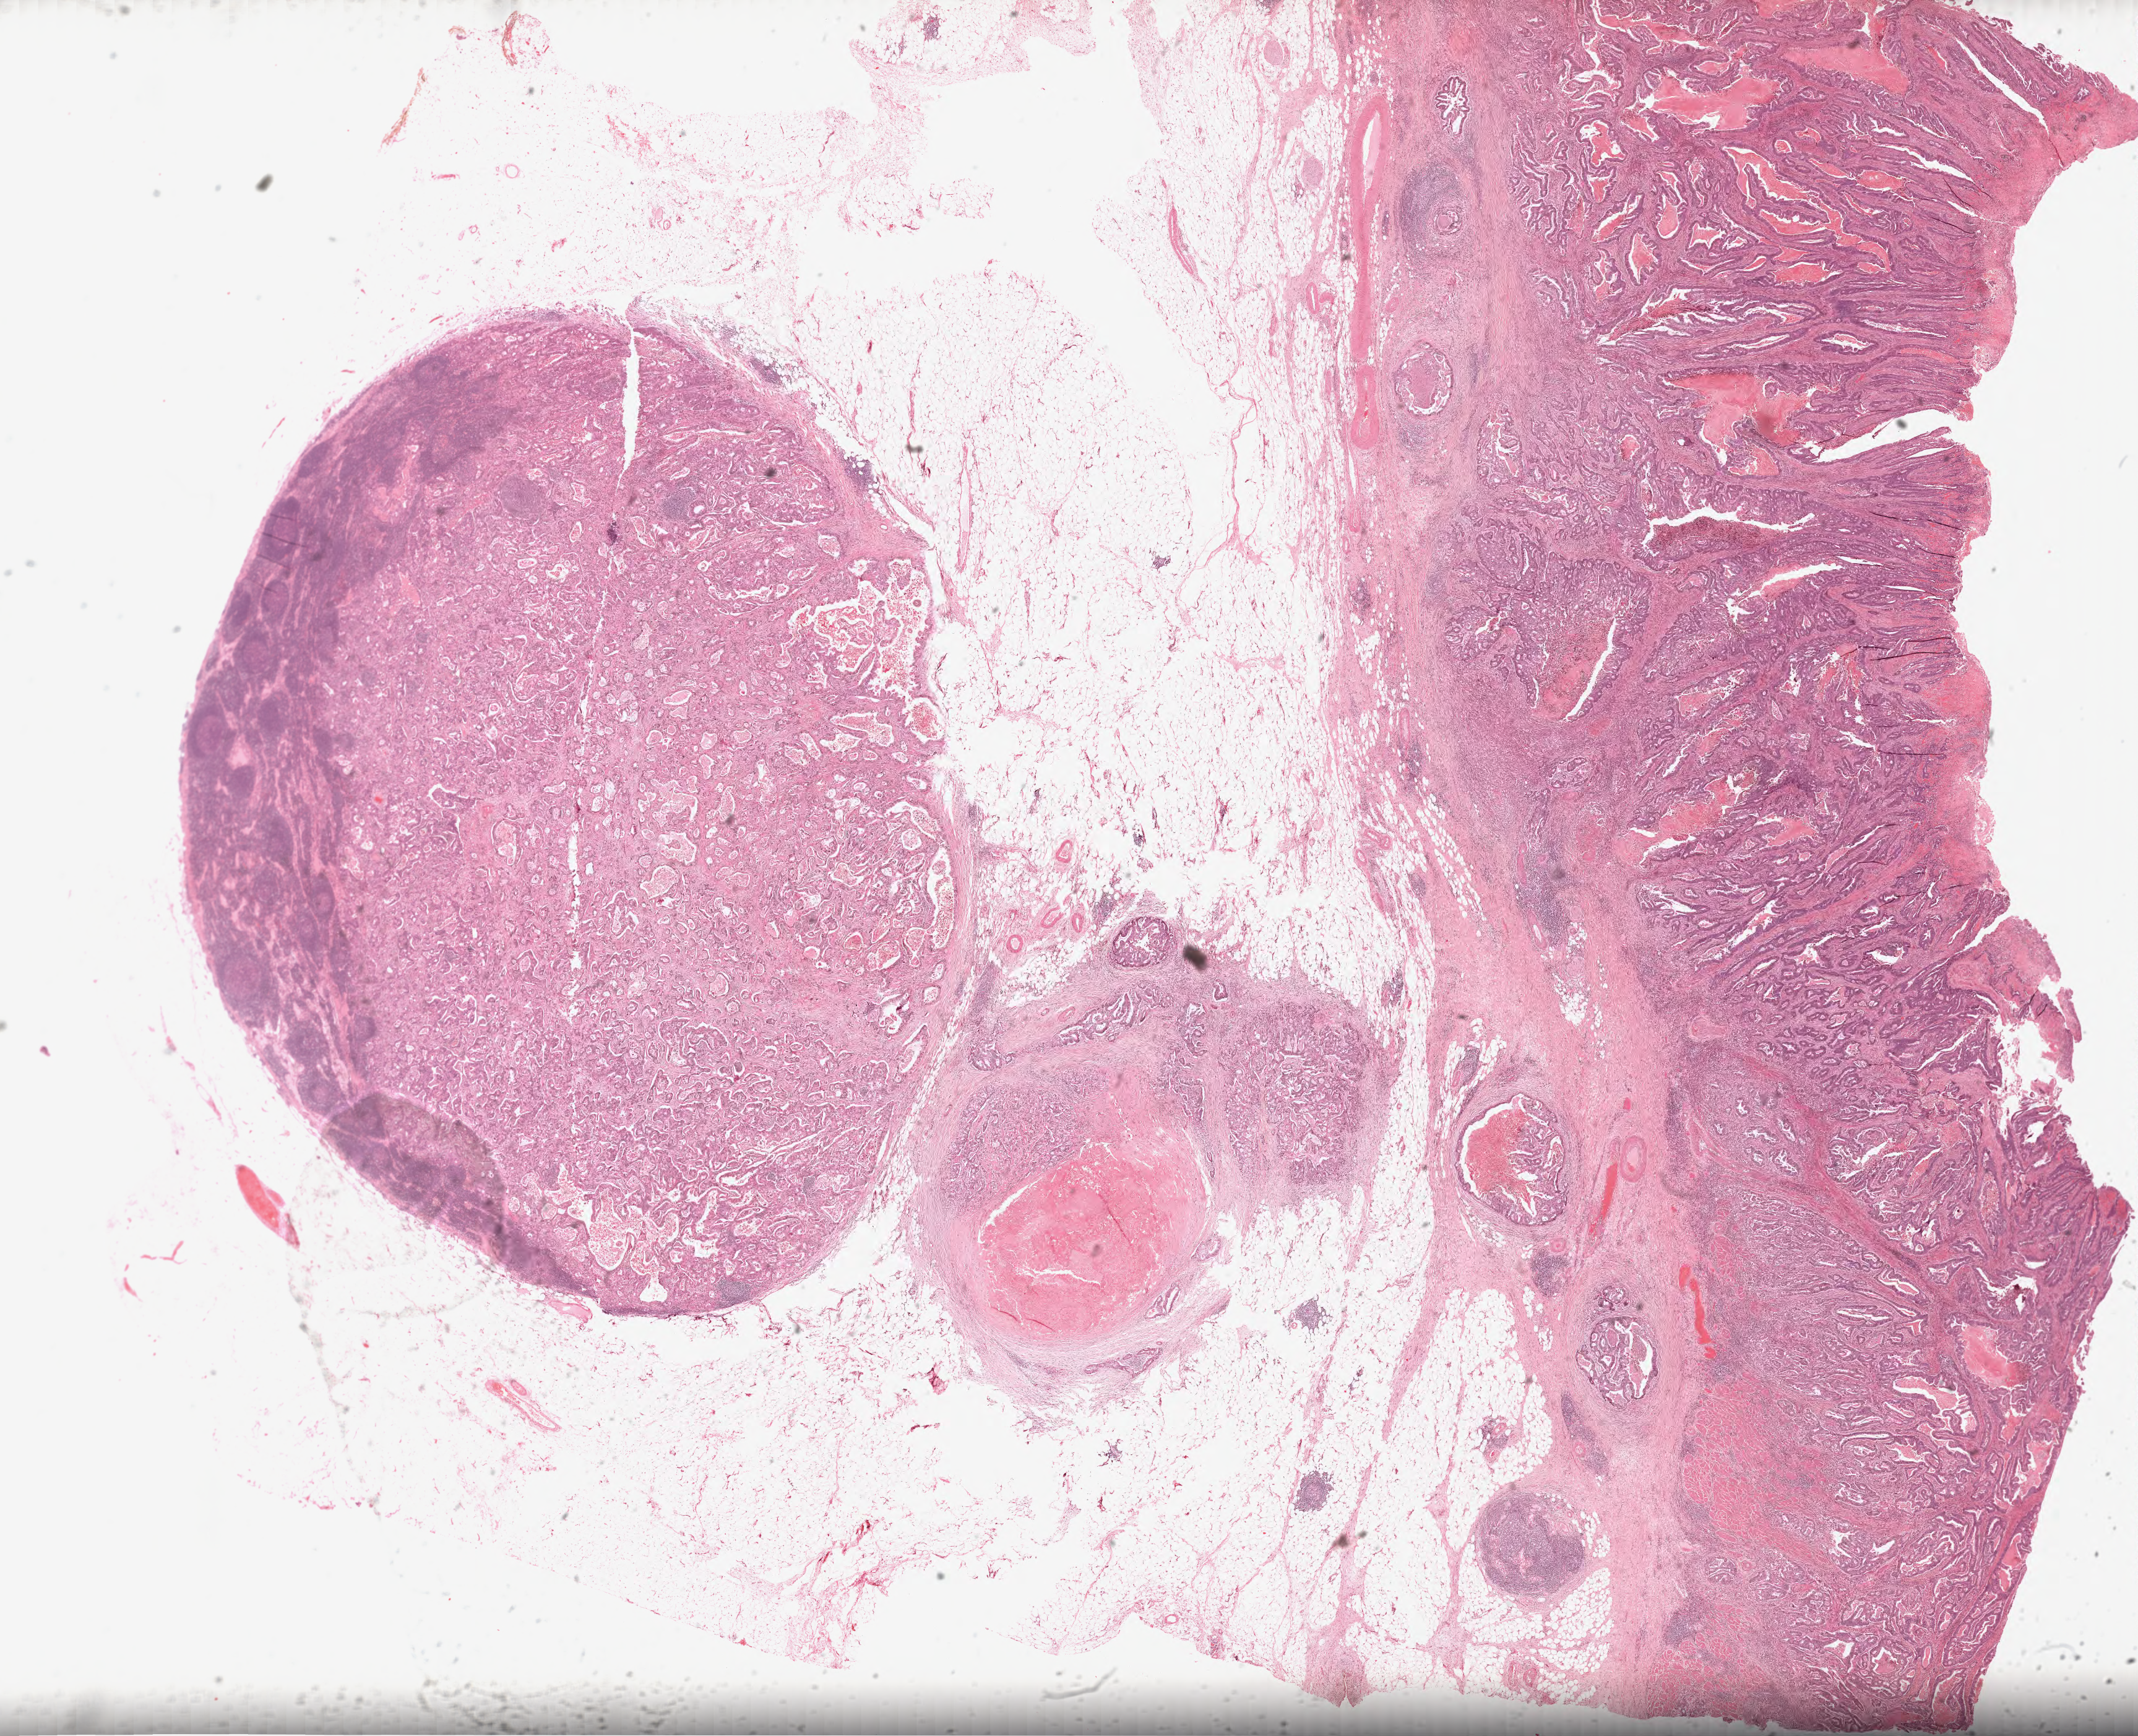
Whole-slide histology image, H&E-stained, low-resolution overview of the scanned area, about 27.8 x 22.6 mm. Formalin-fixed paraffin-embedded (FFPE) diagnostic section. Sample: primary tumour, stomach. Male, age 73 years at initial diagnosis. Histologic grade: G3 (poorly differentiated).
Diagnosis: Adenocarcinoma, intestinal type (cardia, NOS). Lymph nodes positive (case pathology): 4 of 16 examined. TNM: T3 N2 M0. AJCC pathologic stage: IIIA (7th edition).